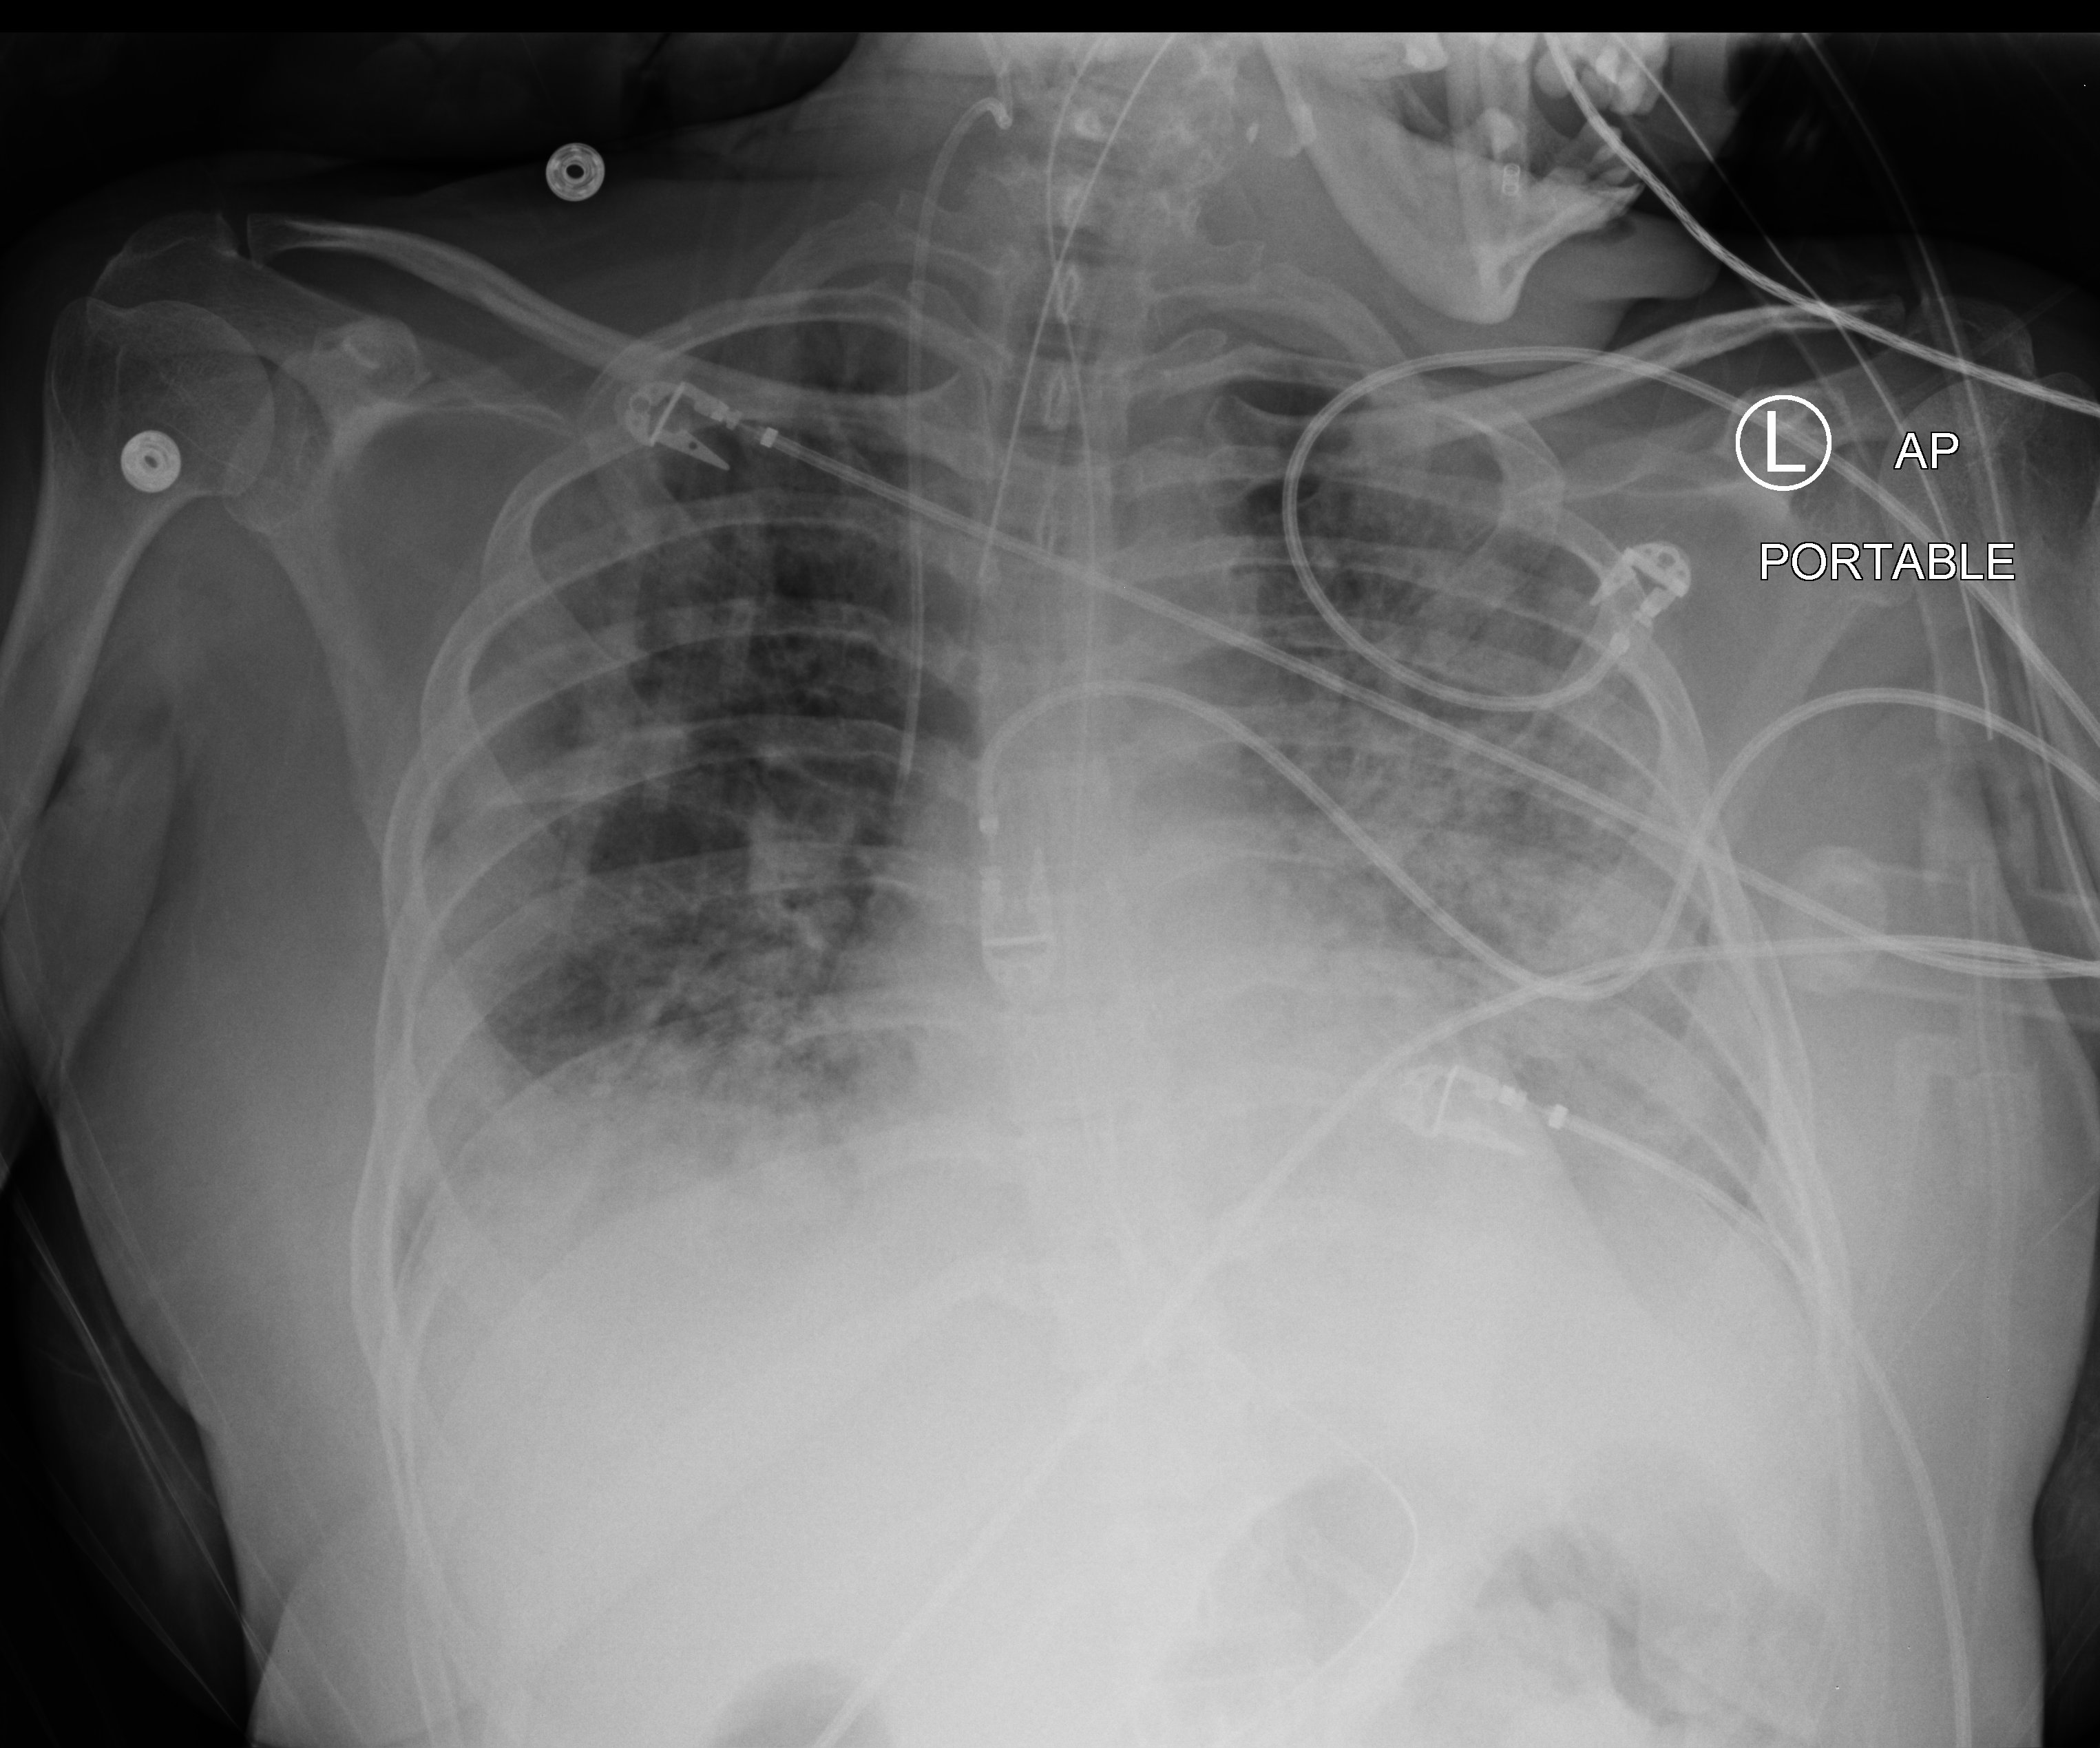
Portable chest radiograph, anteroposterior (AP) projection. Patient hospitalised with COVID-19, aged 18–59 years.
From the hospital-stay record, not from the radiograph (when in the stay this image was taken is not recorded): mechanically ventilated during this hospital stay: yes.